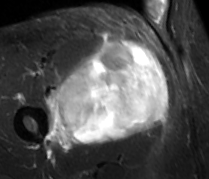
MRI of an extremity soft-tissue mass, one axial slice; slice 47 of 89 in the series (ordered by position); STIR; MR volume resampled by the dataset authors to the PET/CT grid (not the native acquisition matrix); 209 × 179 image matrix, field of view 204 × 175 mm. Male patient. From the clinical record (not read from this slice): histological type: undifferentiated - pleiomorphic; grade: high; site of the primary tumour: right thigh.
Outlined on this slice (expert contour drawn on MRI and transferred to this co-registered scan by the dataset authors):
- gross tumour volume including surrounding oedema: bounding box <44,37,168,149> (left, top, right, bottom; pixels)
- gross tumour volume (mass): <55,39,168,145>